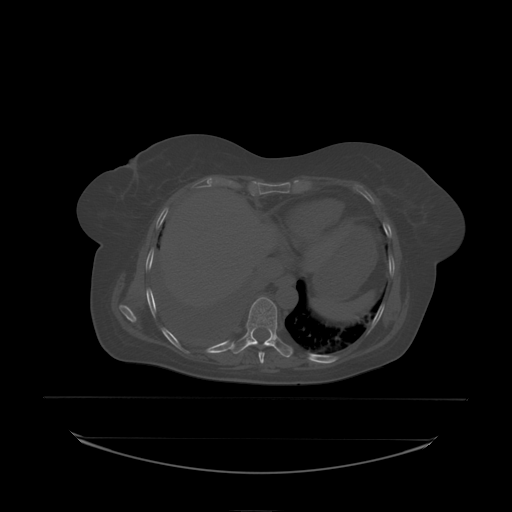
CT including the spine, one axial slice; position 125 of 242 along the scan axis; bone window (W 1800 / L 400 HU); 2.5 mm slice thickness; 512 × 512 image matrix, field of view 500 × 500 mm. Female patient, age 53 years. Case-level facts recorded for this patient, not image findings: primary cancer: lung; vertebrae with lytic lesions (as recorded): T7, L1.
Annotated regions visible in this slice (semi-automatically segmented with operator editing):
- T9 vertebra: box from (x=245, y=297) to (x=278, y=338) px